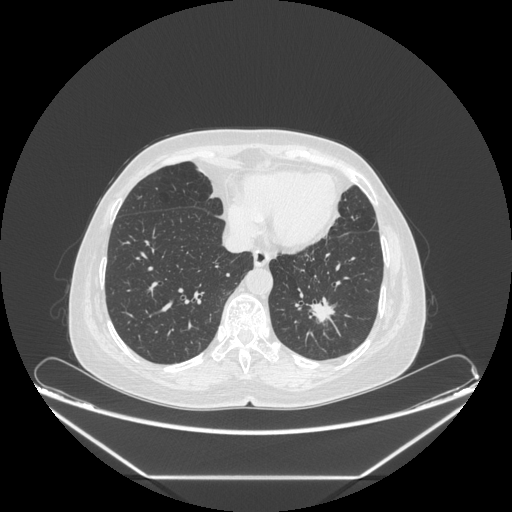
Chest CT, one axial slice; slice 75 of 241 in the series (ordered by position); reconstruction kernel STANDARD; lung window (W 1500 / L -600 HU); 1.25 mm slice thickness; 512 × 512 image matrix, field of view 451 × 451 mm. Patient: female, 63 years. From the clinical record (not read from this slice): clinical TNM (as recorded): T1c N0 M0.
Annotated regions visible in this slice (bounding box drawn by a radiologist):
- lung tumour (recorded histology: adenocarcinoma): bounding box [x1, y1, x2, y2] px = [302, 284, 344, 335]